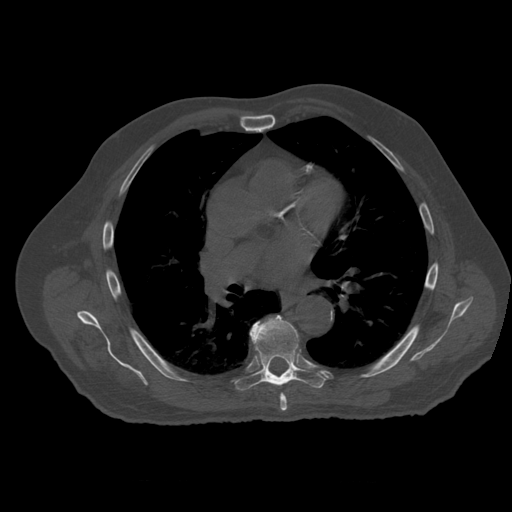
CT including the spine, one axial slice; position 367 of 399 along the scan axis; reconstruction kernel STANDARD; bone window (W 1800 / L 400 HU); 512 × 512 image matrix, field of view 407 × 407 mm. Patient age 73 years. From the clinical record (not read from this slice): primary cancer: prostate.
Outlined on this slice (semi-automatically segmented with operator editing):
- T6 vertebra: bounding box (x1, y1, x2, y2) in pixels: (280, 394, 288, 413)
- T7 vertebra: (236, 315, 327, 391)